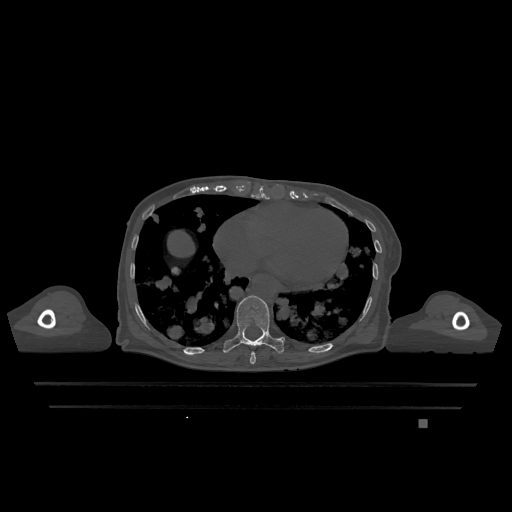
CT including the spine, one axial slice. Slice 649 of 1317 in the series (ordered by position). Bone window (W 1800 / L 400 HU). 512 × 512 image matrix, field of view 500 × 500 mm. Patient: female, 74 years. From the clinical record (not read from this slice): primary cancer: lung; vertebrae with lytic lesions (as recorded): T1, T4, T5, T6, L4, L5.
Structures marked on this image (semi-automatic segmentation, software-assisted and operator-edited):
- T10 vertebra: bounding box (x1, y1, x2, y2) in pixels: (223, 295, 284, 354)
- T9 vertebra: (250, 352, 256, 364)